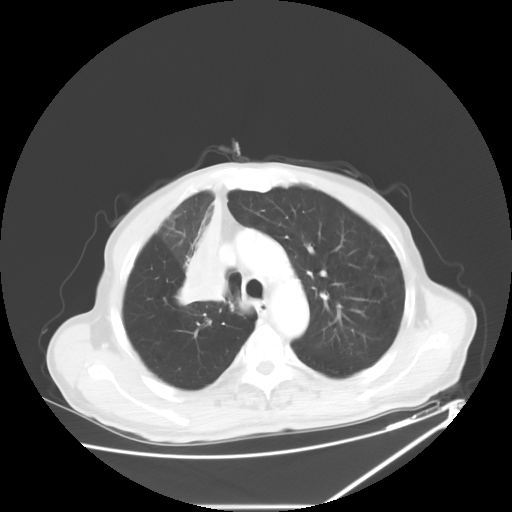
Chest CT, one axial slice. Slice 45 of 60 in the series (ordered by position). Reconstruction kernel STANDARD. 120 kVp. Lung window (W 1500 / L -600 HU). 512 × 512 image matrix. Male patient, age 73 years. From the clinical record (not read from this slice): clinical TNM (as recorded): T2a N1 M0.
Annotated regions visible in this slice (rectangle marked by the reading radiologist):
- lung tumour (recorded histology: squamous cell carcinoma): box from (x=171, y=196) to (x=227, y=309) px